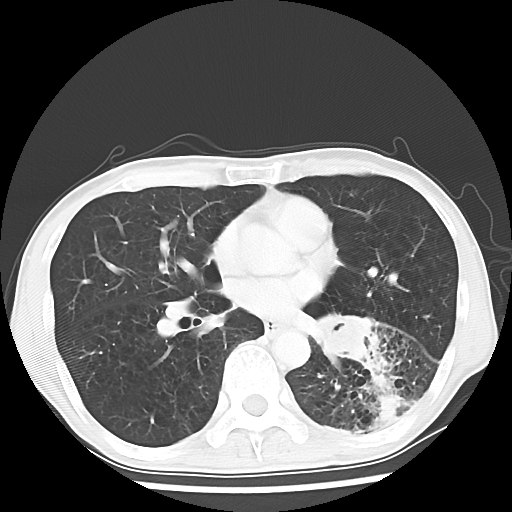
Chest CT, one axial slice. Slice 30 of 64 in the series (ordered by position). Reconstruction kernel LUNG. Lung window (W 1500 / L -600 HU). 5 mm slice thickness. 512 × 512 image matrix, field of view 313 × 313 mm. Male patient, age 68 years. Case-level facts recorded for this patient, not image findings: clinical TNM (as recorded): T4 N0 M0.
Annotated regions visible in this slice (rectangle marked by the reading radiologist):
- lung tumour (recorded histology: squamous cell carcinoma): box from (x=291, y=306) to (x=371, y=360) px